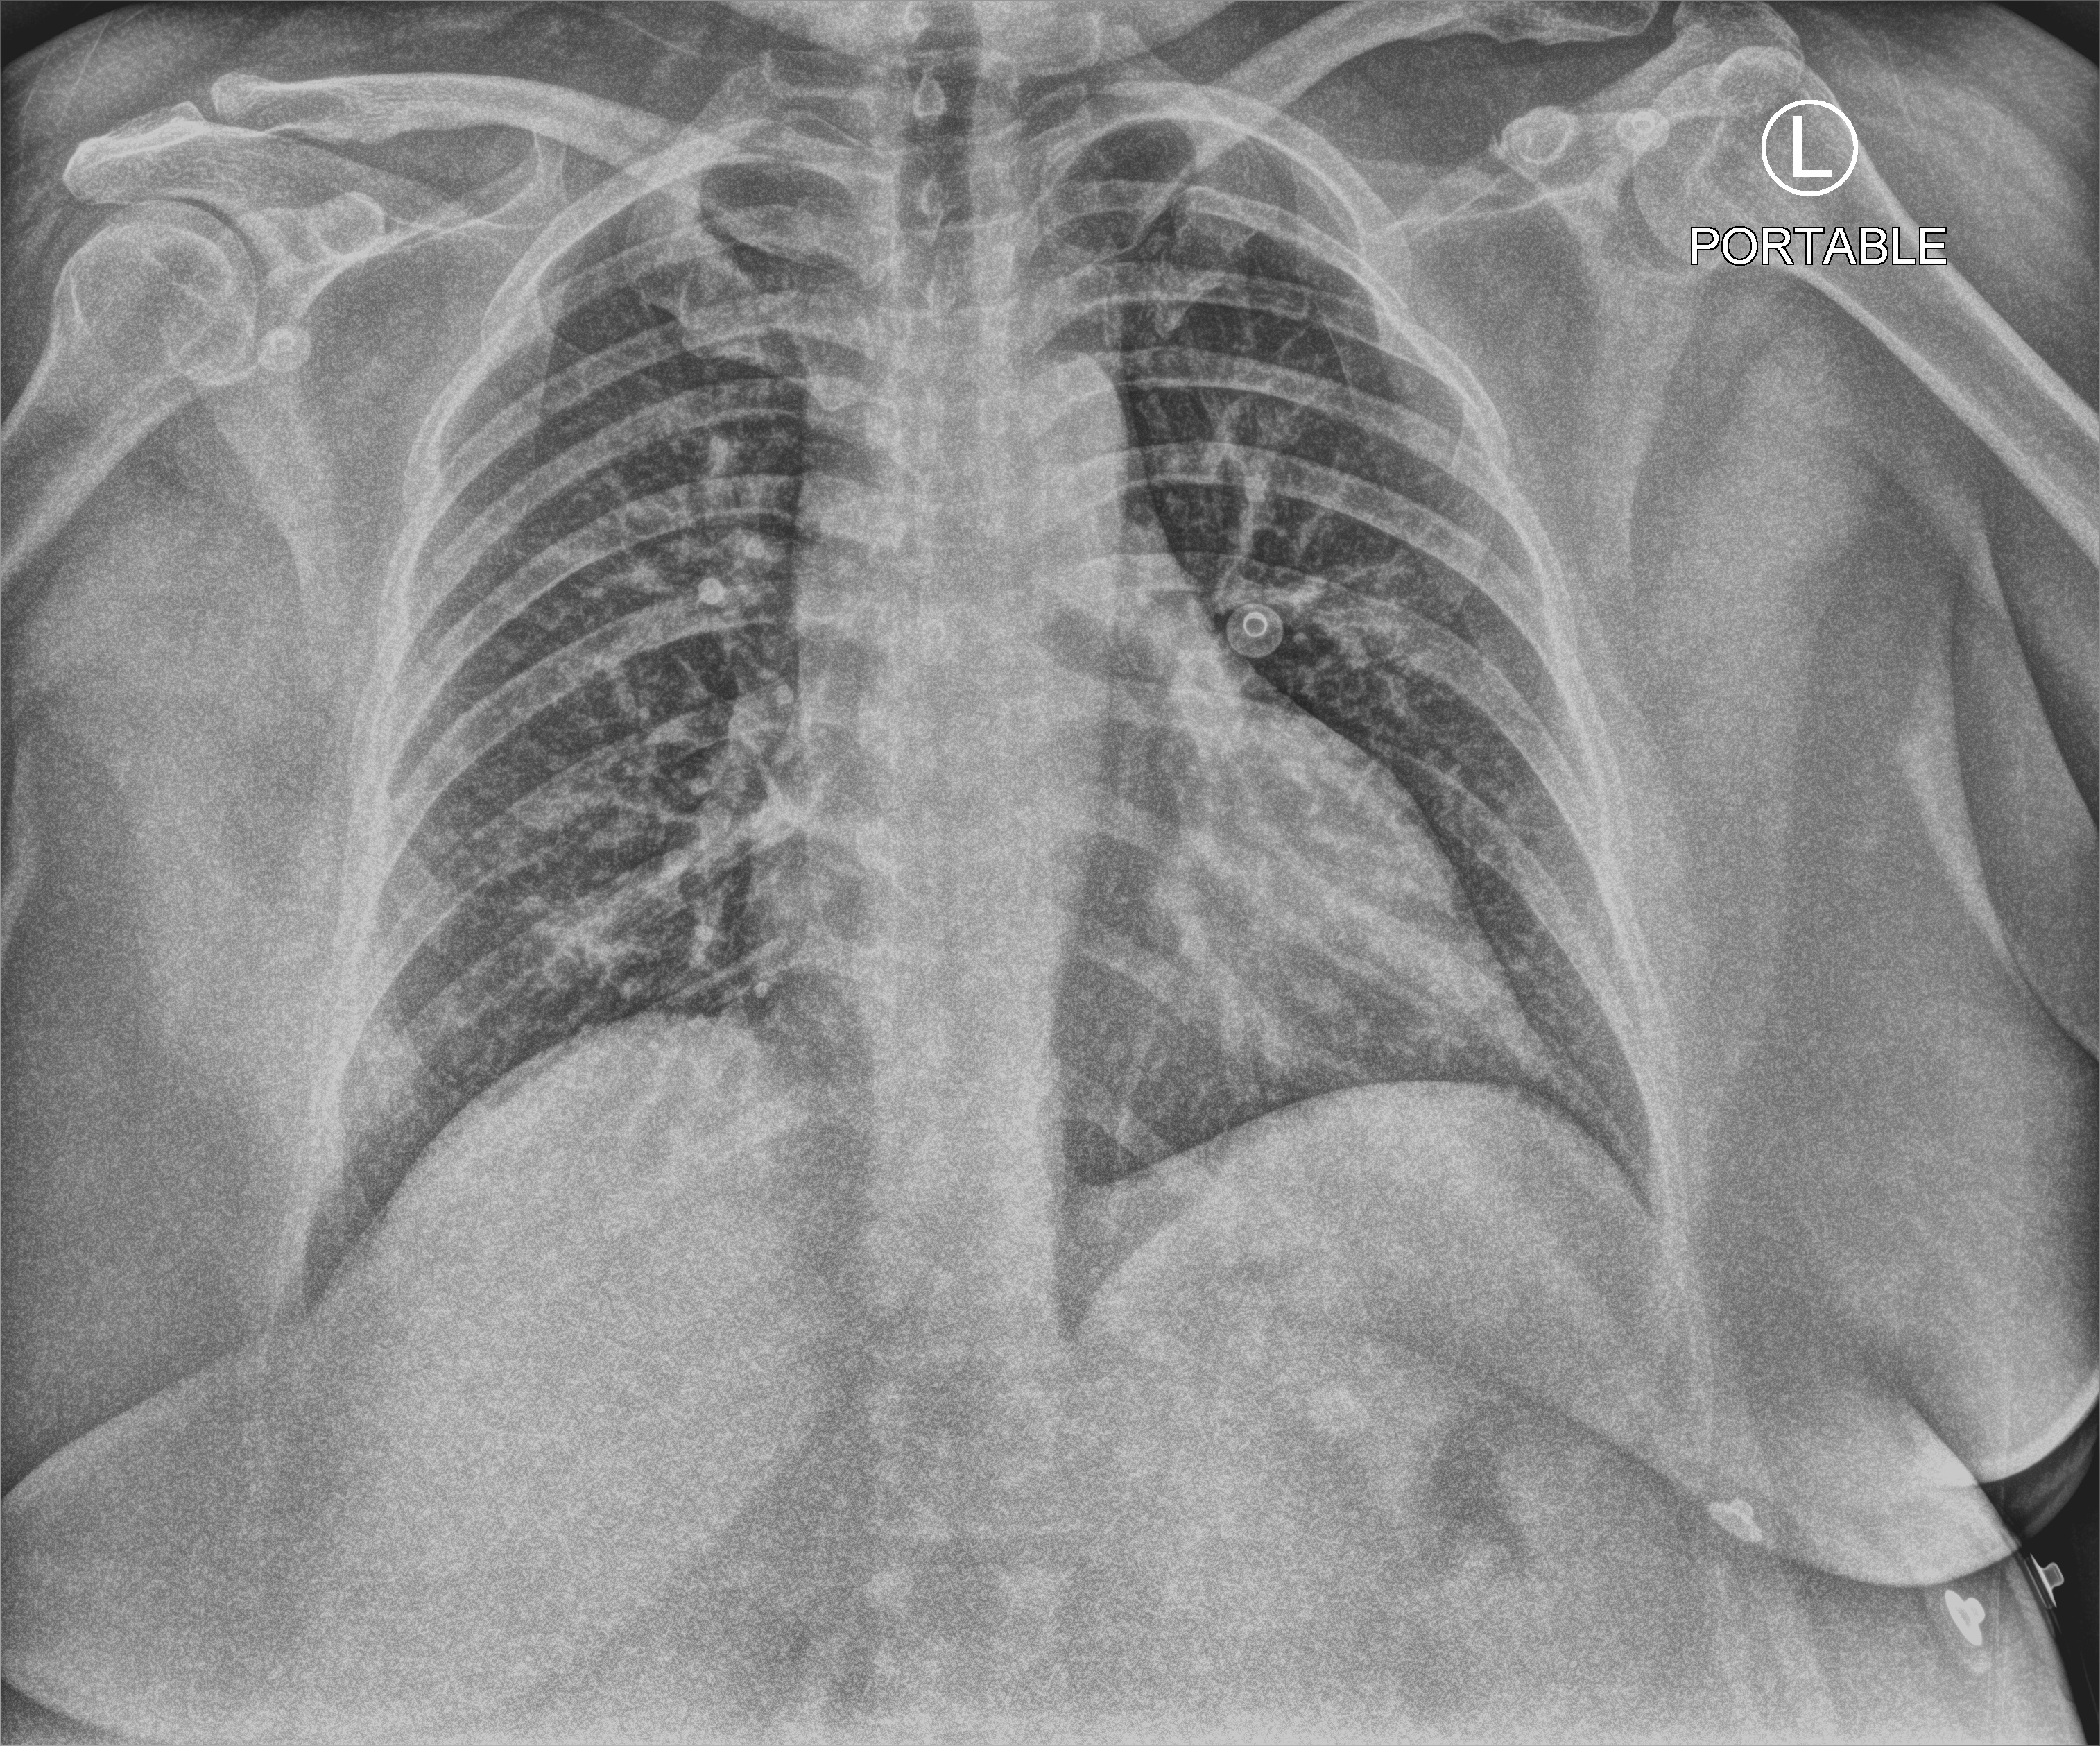
Portable chest radiograph; anteroposterior (AP) projection. Female patient hospitalised with COVID-19, age 18–59 years.
From the hospital-stay record, not from the radiograph (when in the stay this image was taken is not recorded): COPD (admission record): no.